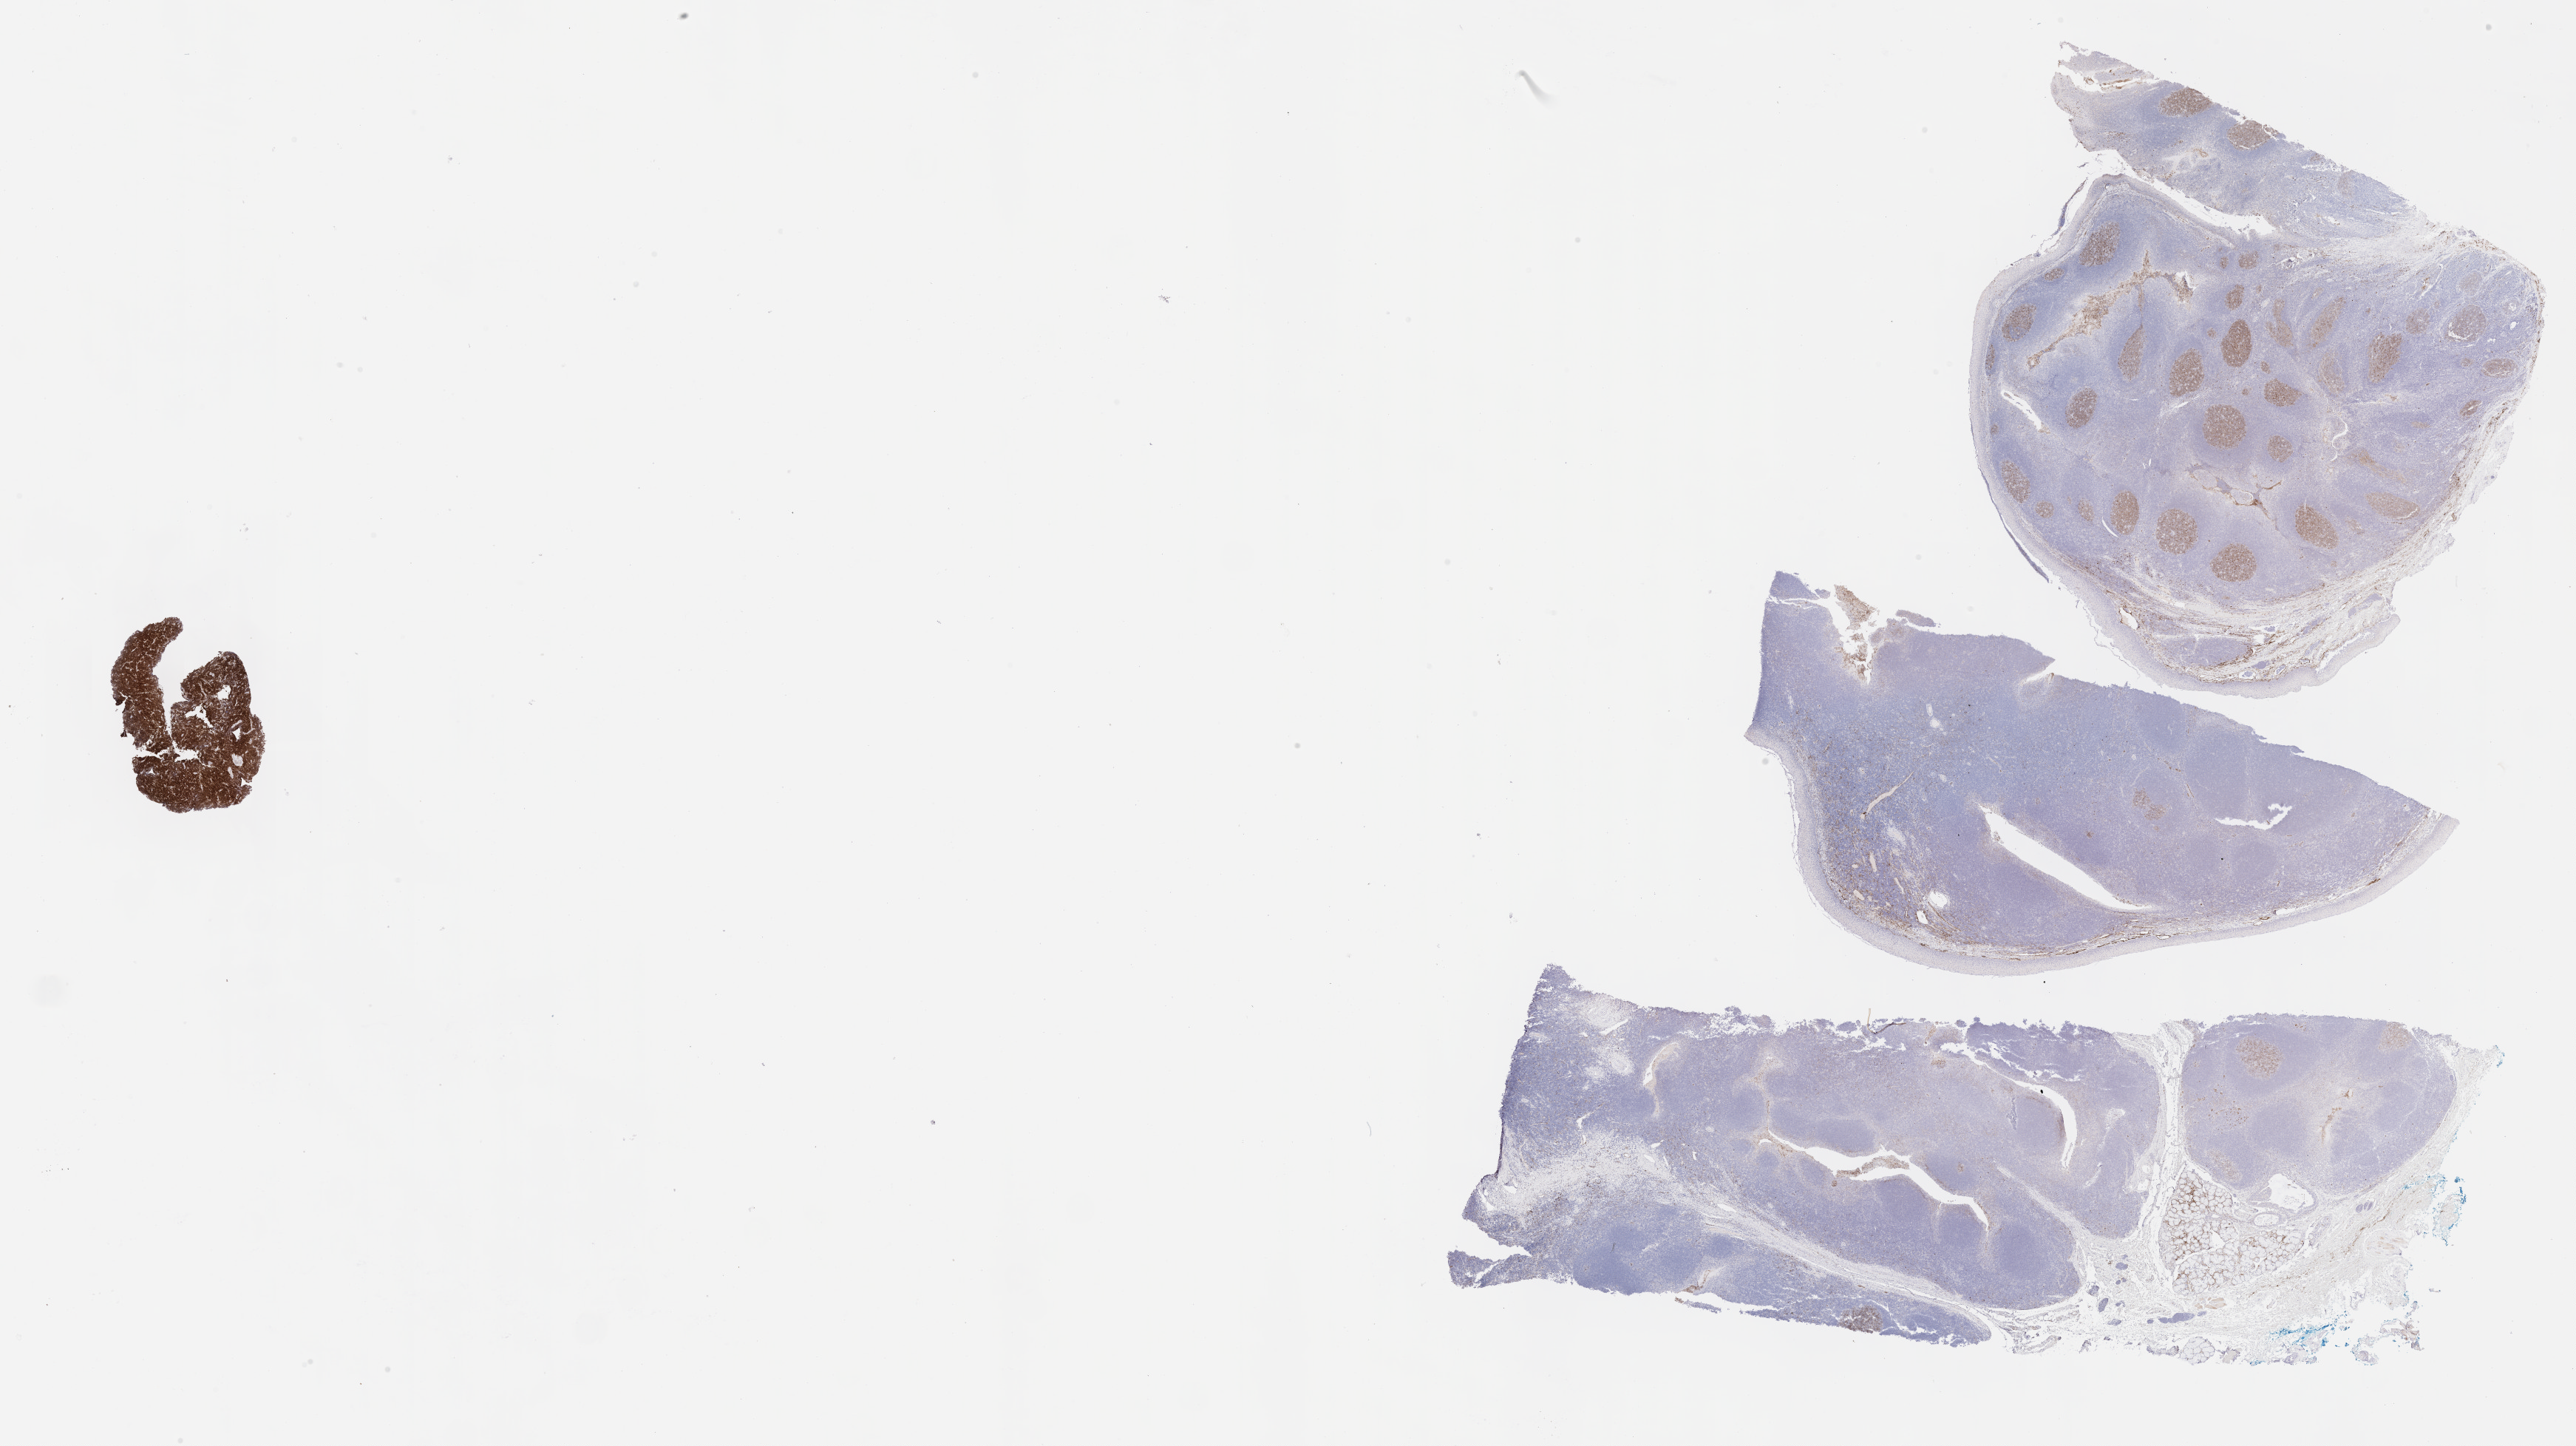
Immunohistochemistry (IHC) whole-slide image stained for CD10, a low-resolution overview of the entire scanned area, about 28.2 x 15.8 mm. Specimen: tumor tissue. Female, age 8 years at initial diagnosis.
Histologic diagnosis: Burkitt lymphoma, NOS.